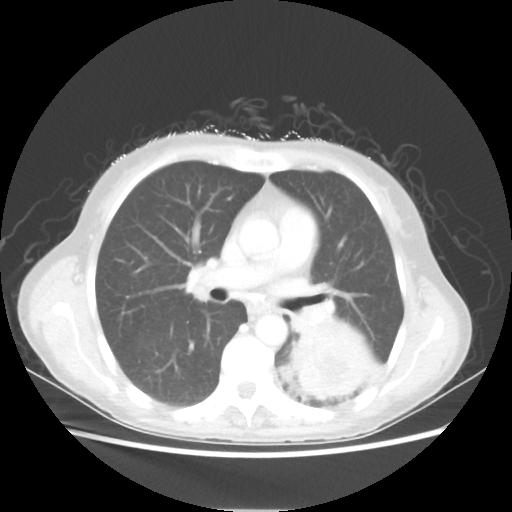
Chest CT, one axial slice. Slice 32 of 56 in the series (ordered by position). Lung window (W 1500 / L -600 HU). 512 × 512 image matrix. Patient: female, 53 years. From the clinical record (not read from this slice): clinical TNM (as recorded): T3 N0 M0.
Annotated regions visible in this slice (bounding box drawn by a radiologist):
- lung tumour (recorded histology: adenocarcinoma): box from (x=279, y=296) to (x=388, y=400) px